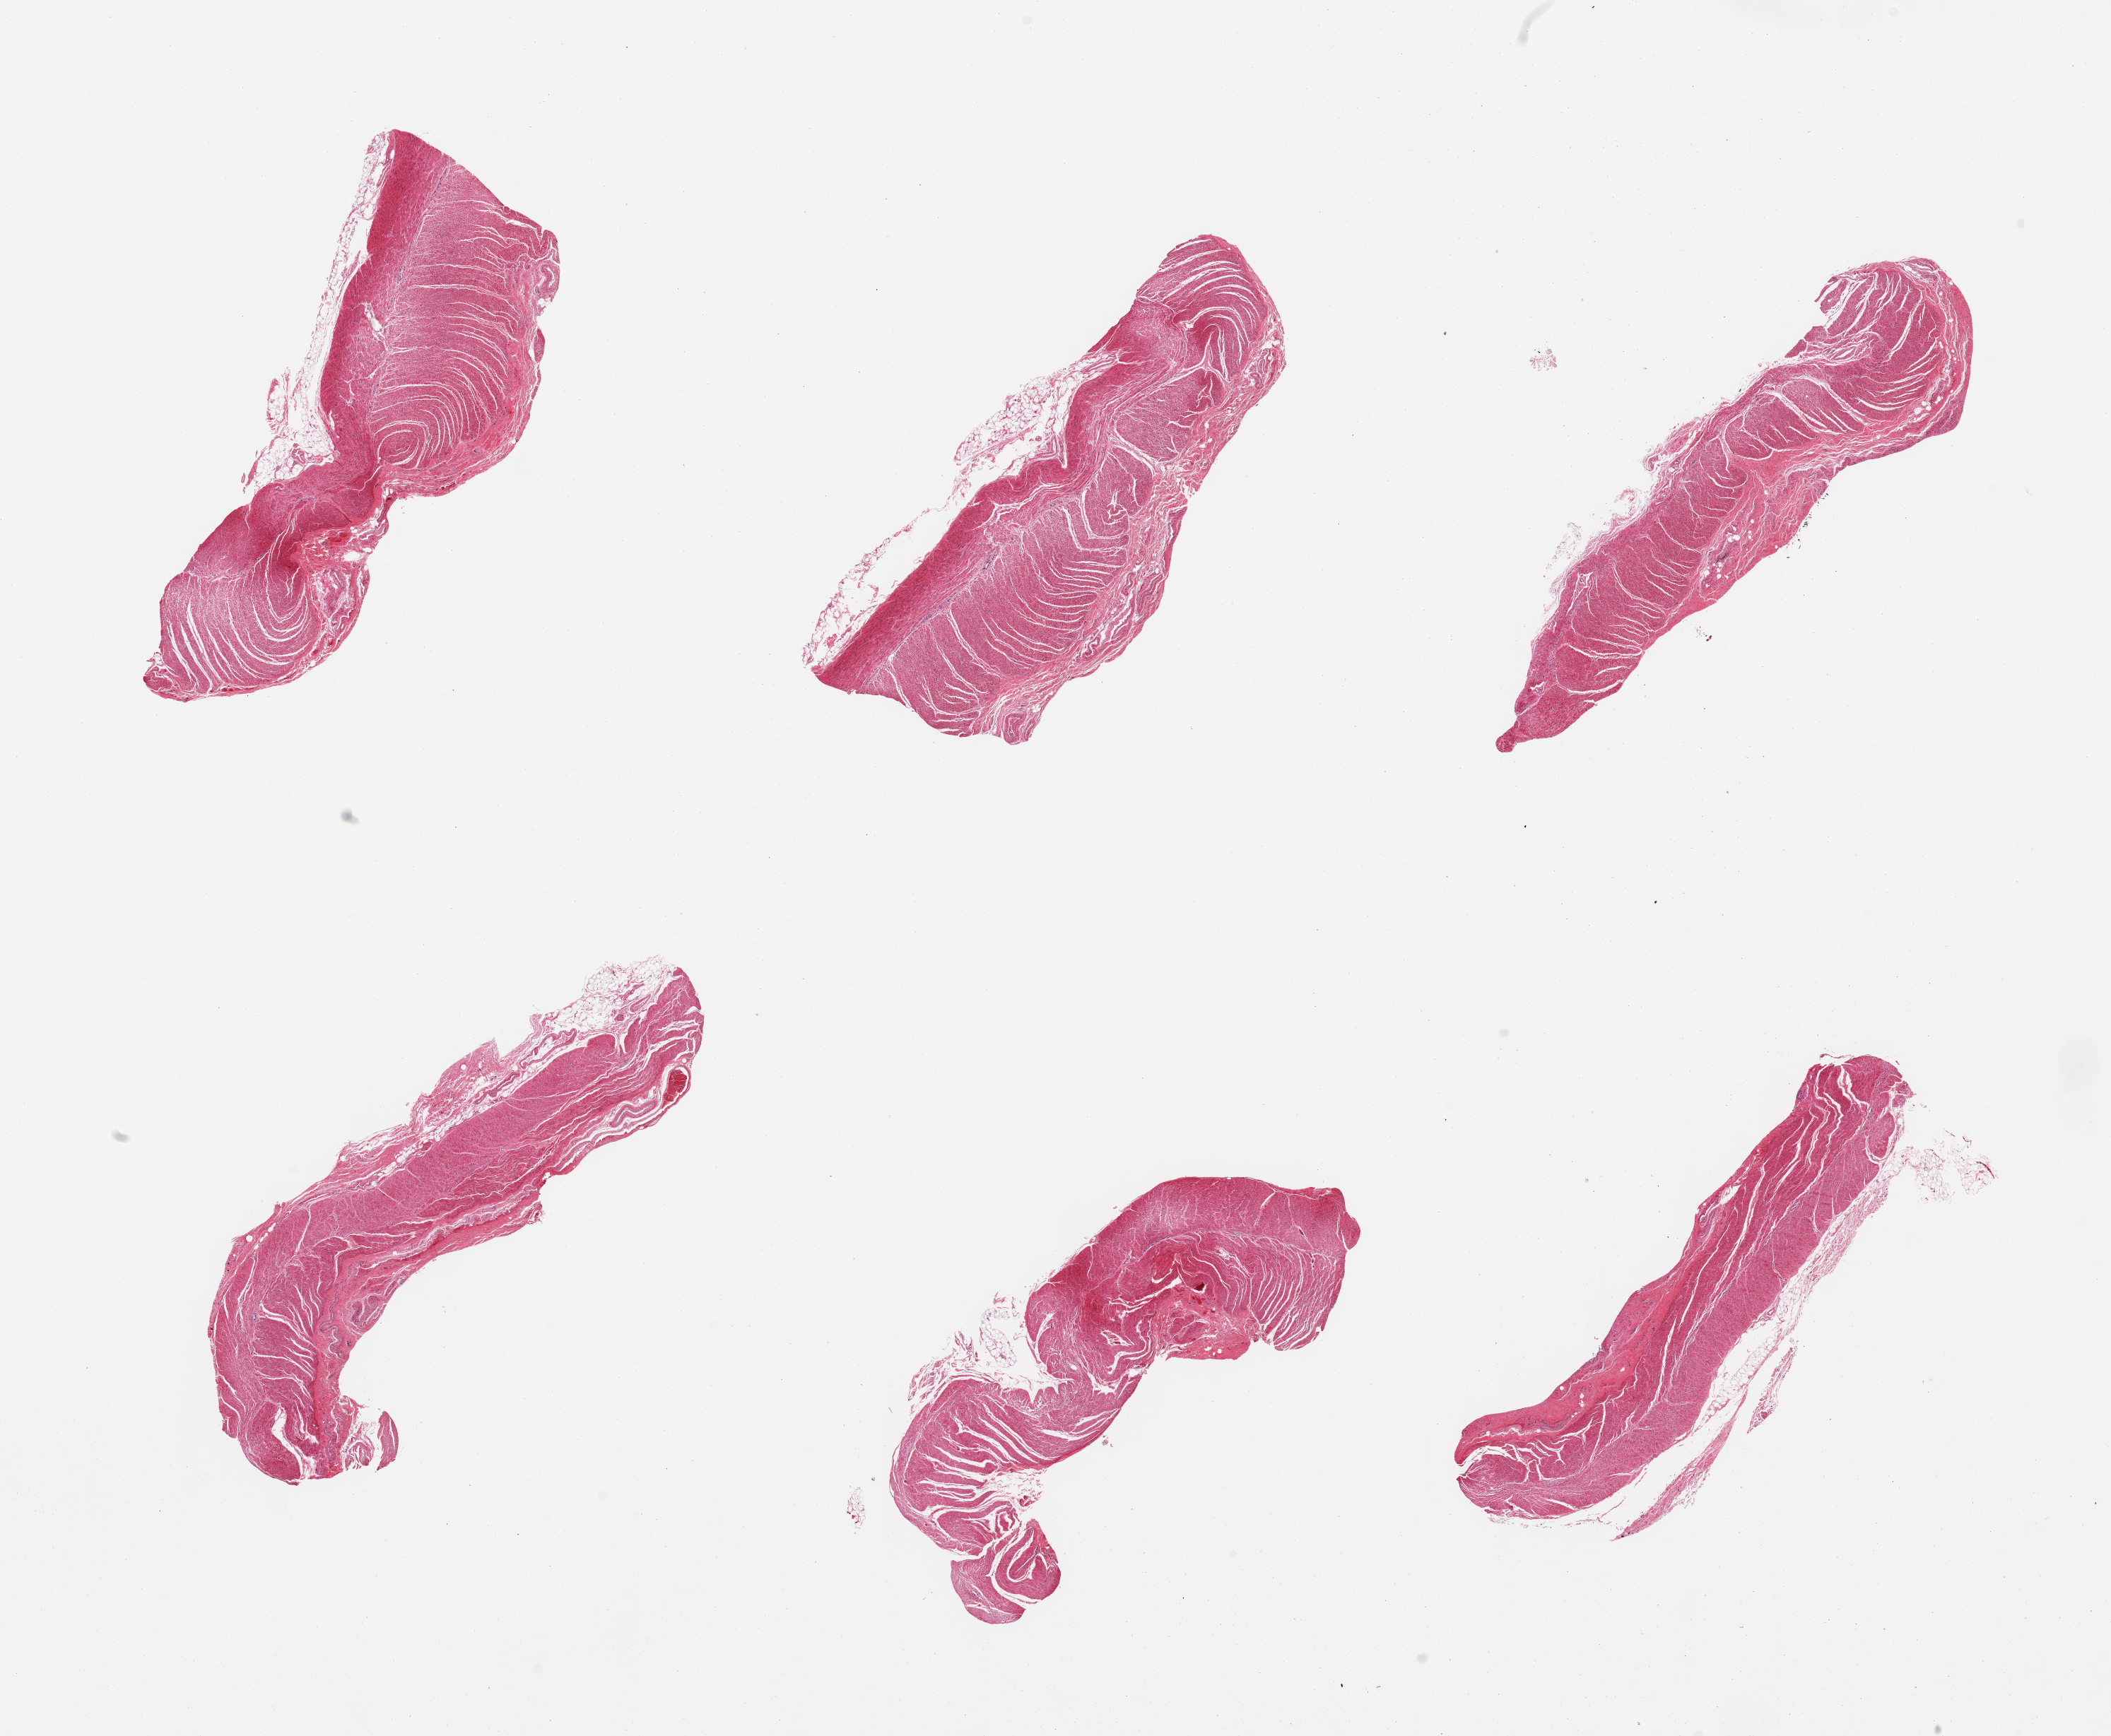
Whole-slide image, hematoxylin and eosin (H&E) stain, brightfield, shown as a low-resolution overview of the whole scanned area (about 23.6 x 19.4 mm), PAXgene-fixed, paraffin-embedded tissue, sampled site (target tissue): sigmoid colon, tissue donor sample. Donor sex: male.
- reviewer comment on this tissue sample: 6 pieces, all target muscularis